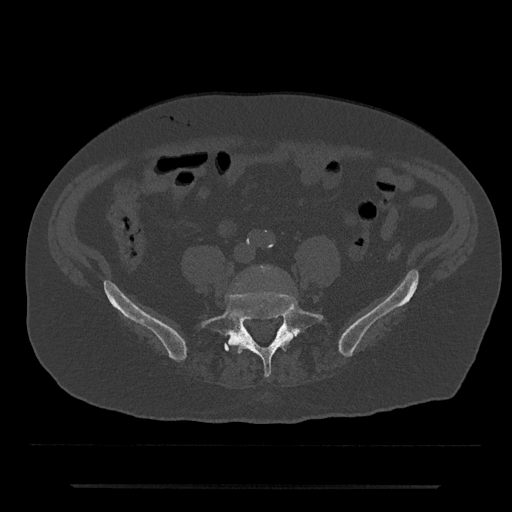
CT including the spine, one axial slice; slice 298 of 797 in the series (ordered by position); bone window (W 1800 / L 400 HU); 512 × 512 image matrix. Male patient, age 80 years. From the clinical record (not read from this slice): primary cancer: prostate; vertebrae with lytic lesions (as recorded): L1, T11.
Outlined on this slice (semi-automatically segmented with operator editing):
- L4 vertebra: bounding box (x1, y1, x2, y2) in pixels: (259, 265, 273, 273)
- L5 vertebra: (201, 292, 323, 377)